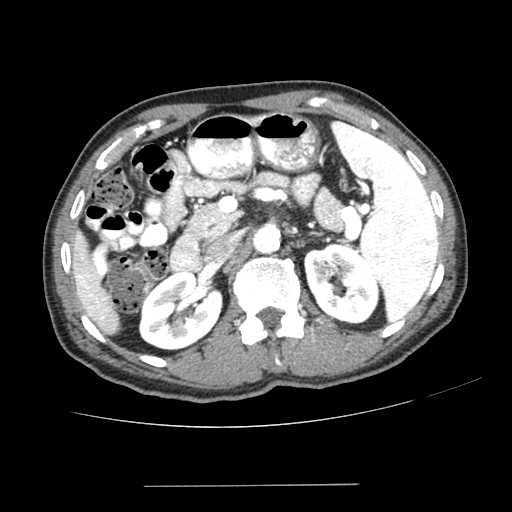
Contrast-enhanced abdominal CT (liver protocol), one axial slice; position 138 of 187 along the scan axis; reconstruction kernel SOFT; 100 kVp; one of 2 acquisitions stored at this slice position; soft-tissue window (W 400 / L 40 HU); 2.5 mm slice thickness; 512 × 512 image matrix. Case-level facts recorded for this patient, not image findings: diagnosis: hepatocellular carcinoma (patient treated with transarterial chemoembolisation; whether this scan precedes or follows treatment is not stated here); TNM stage (as recorded): Stage-I.
Annotated regions visible in this slice (semi-automatically segmented with operator editing):
- liver parenchyma outside the tumour (the mass and vessels are separate outlines, so this box may not span the whole liver): bounding box [x1, y1, x2, y2] px = [72, 230, 120, 334]
- liver vessels: [77, 275, 105, 319]